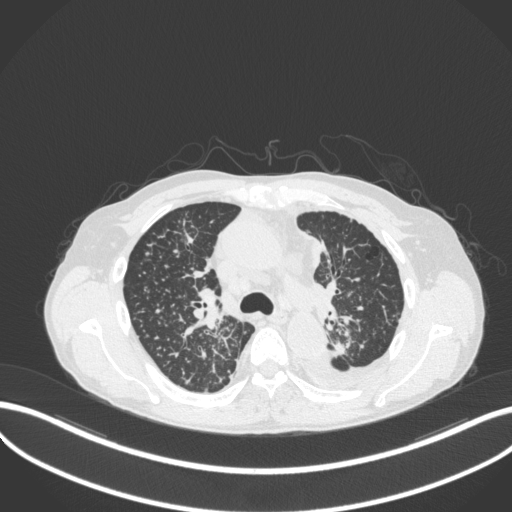
Chest CT, one axial slice. Slice 245 of 319 in the series (ordered by position). 120 kVp. Lung window (W 1500 / L -600 HU). 1 mm slice thickness. 512 × 512 image matrix, field of view 400 × 400 mm. Patient: male, 58 years. Case-level facts recorded for this patient, not image findings: clinical TNM (as recorded): T1c N3 M1.
Outlined on this slice (bounding box drawn by a radiologist):
- lung tumour (recorded histology: adenocarcinoma): bounding box <326,340,351,361> (left, top, right, bottom; pixels)